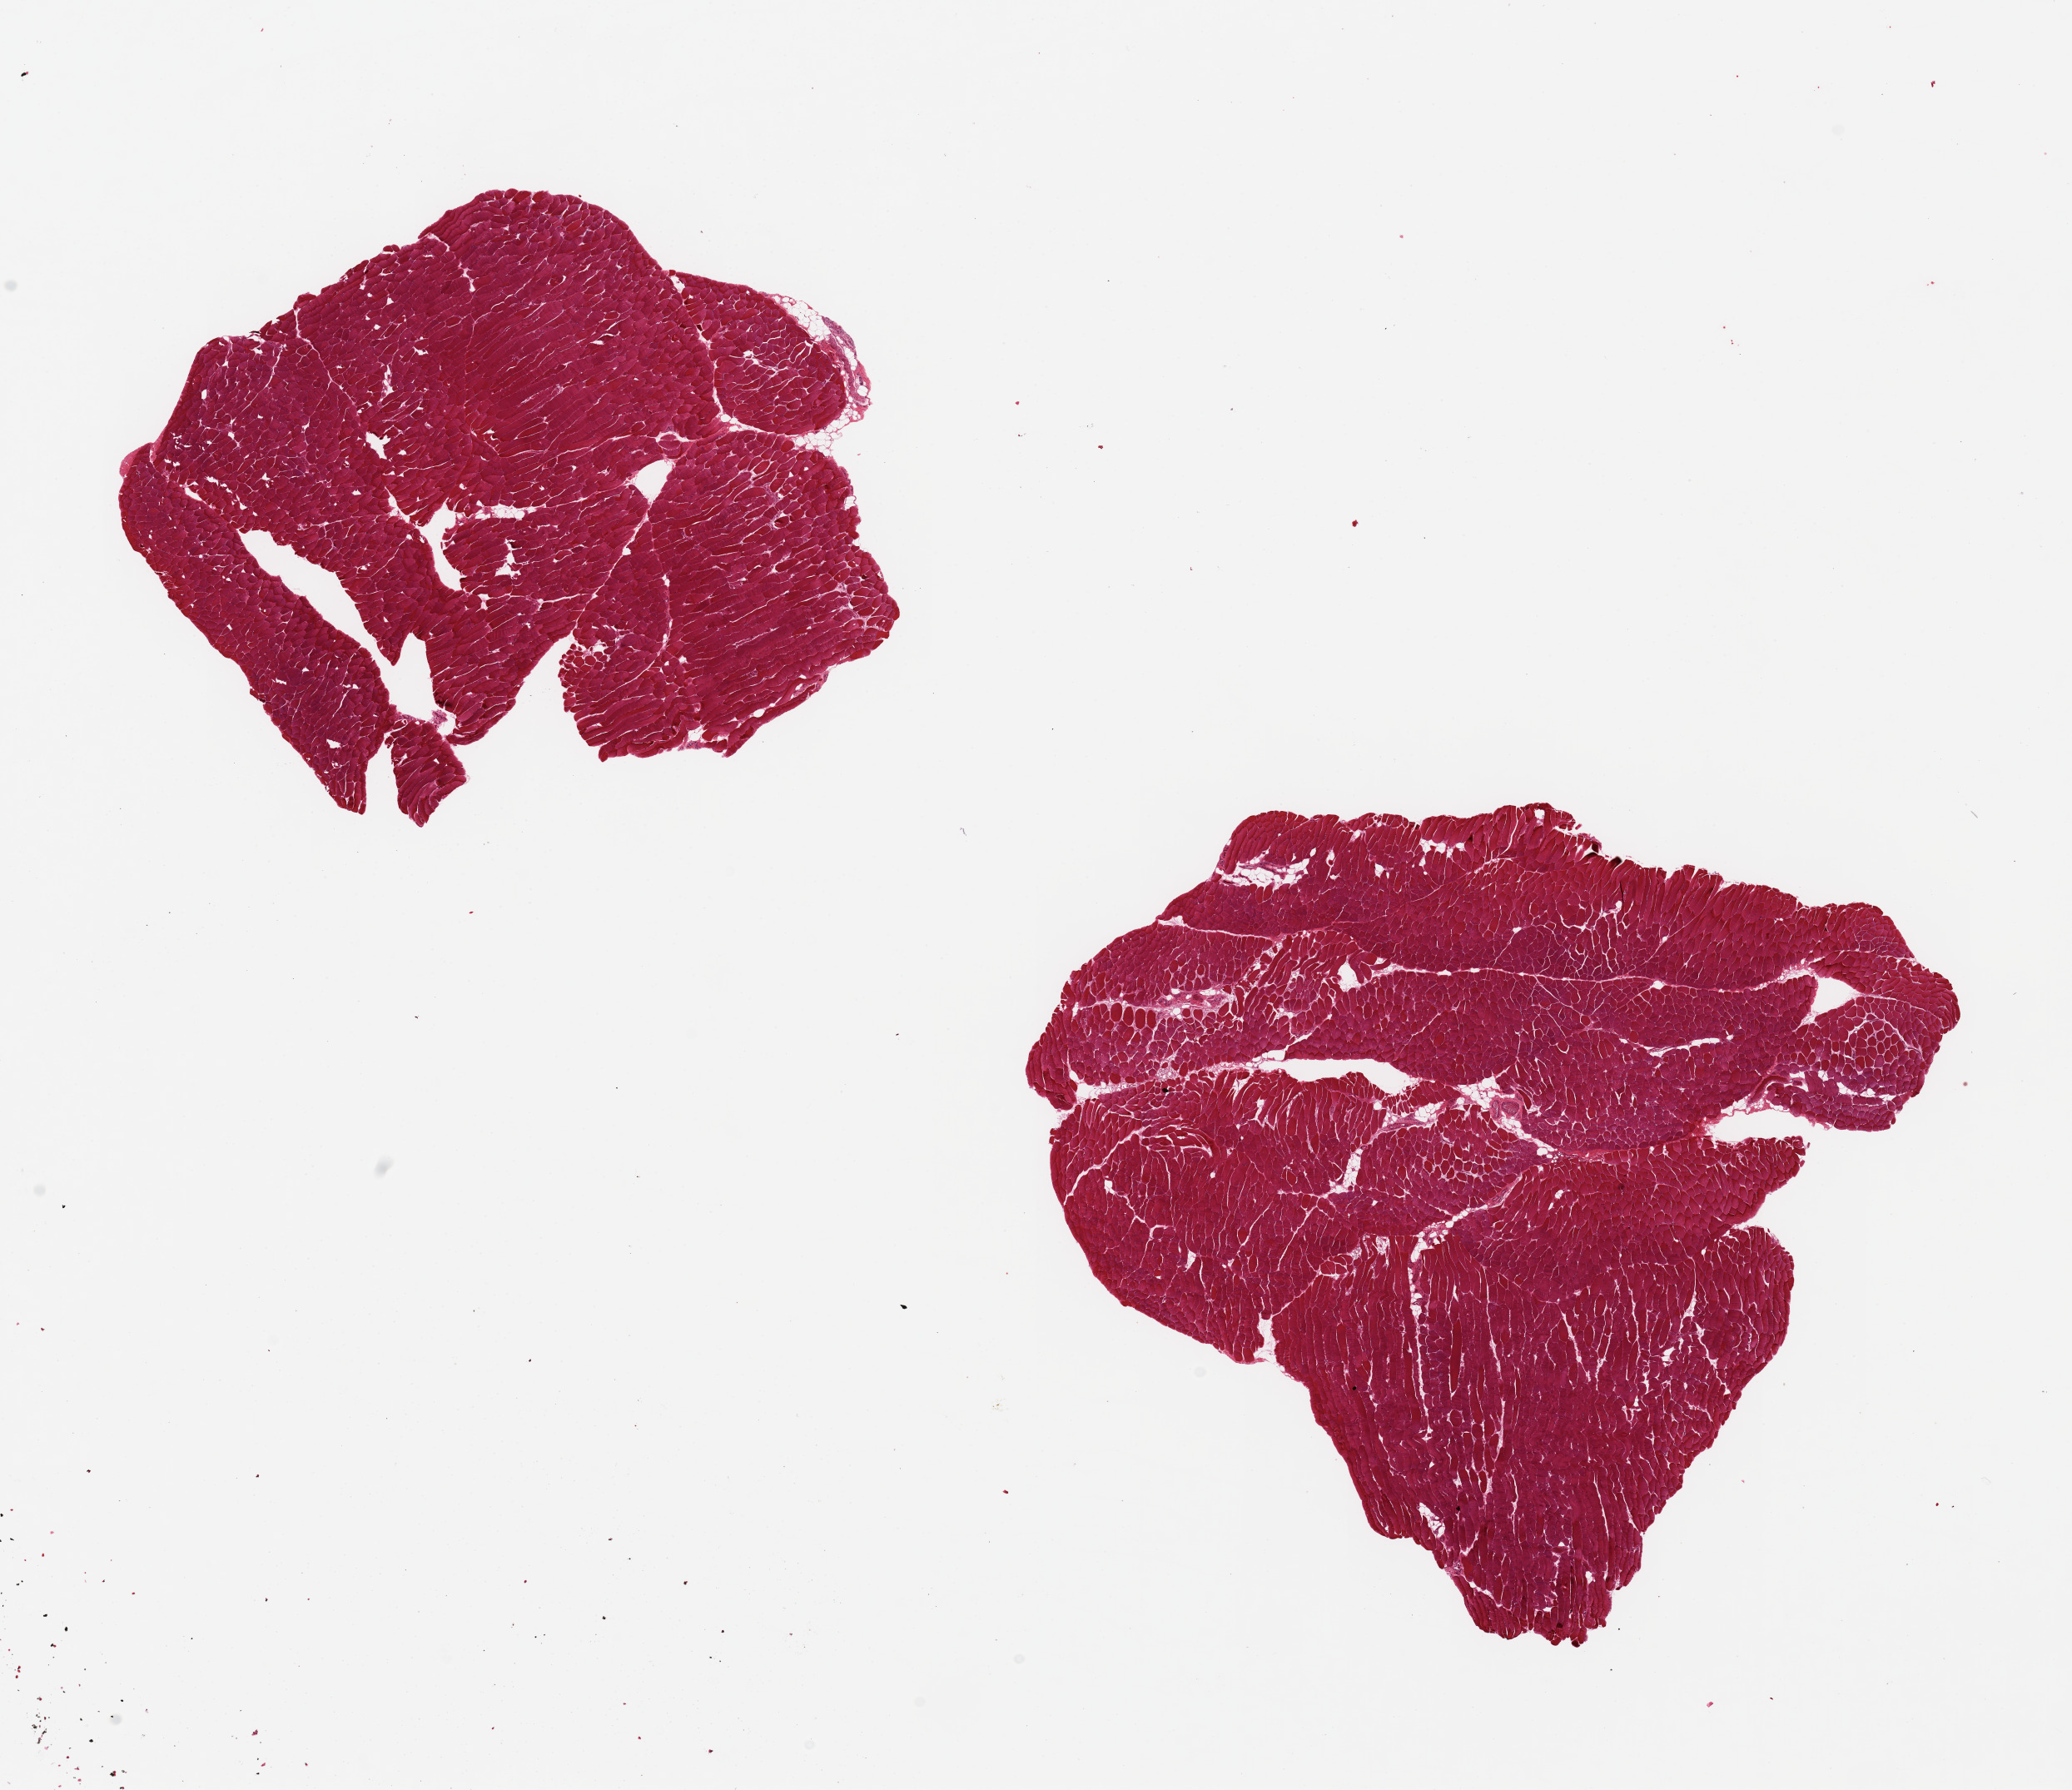
H&E whole-slide image, low-resolution overview of the scanned area, about 19.7 x 17.0 mm, PAXgene-fixed paraffin-embedded (PFPE) section, section of skeletal muscle (target tissue), donor tissue sample. Donor: male.
• review note (as recorded): 2 pieces ~6x6mm, minimal interstitial fat